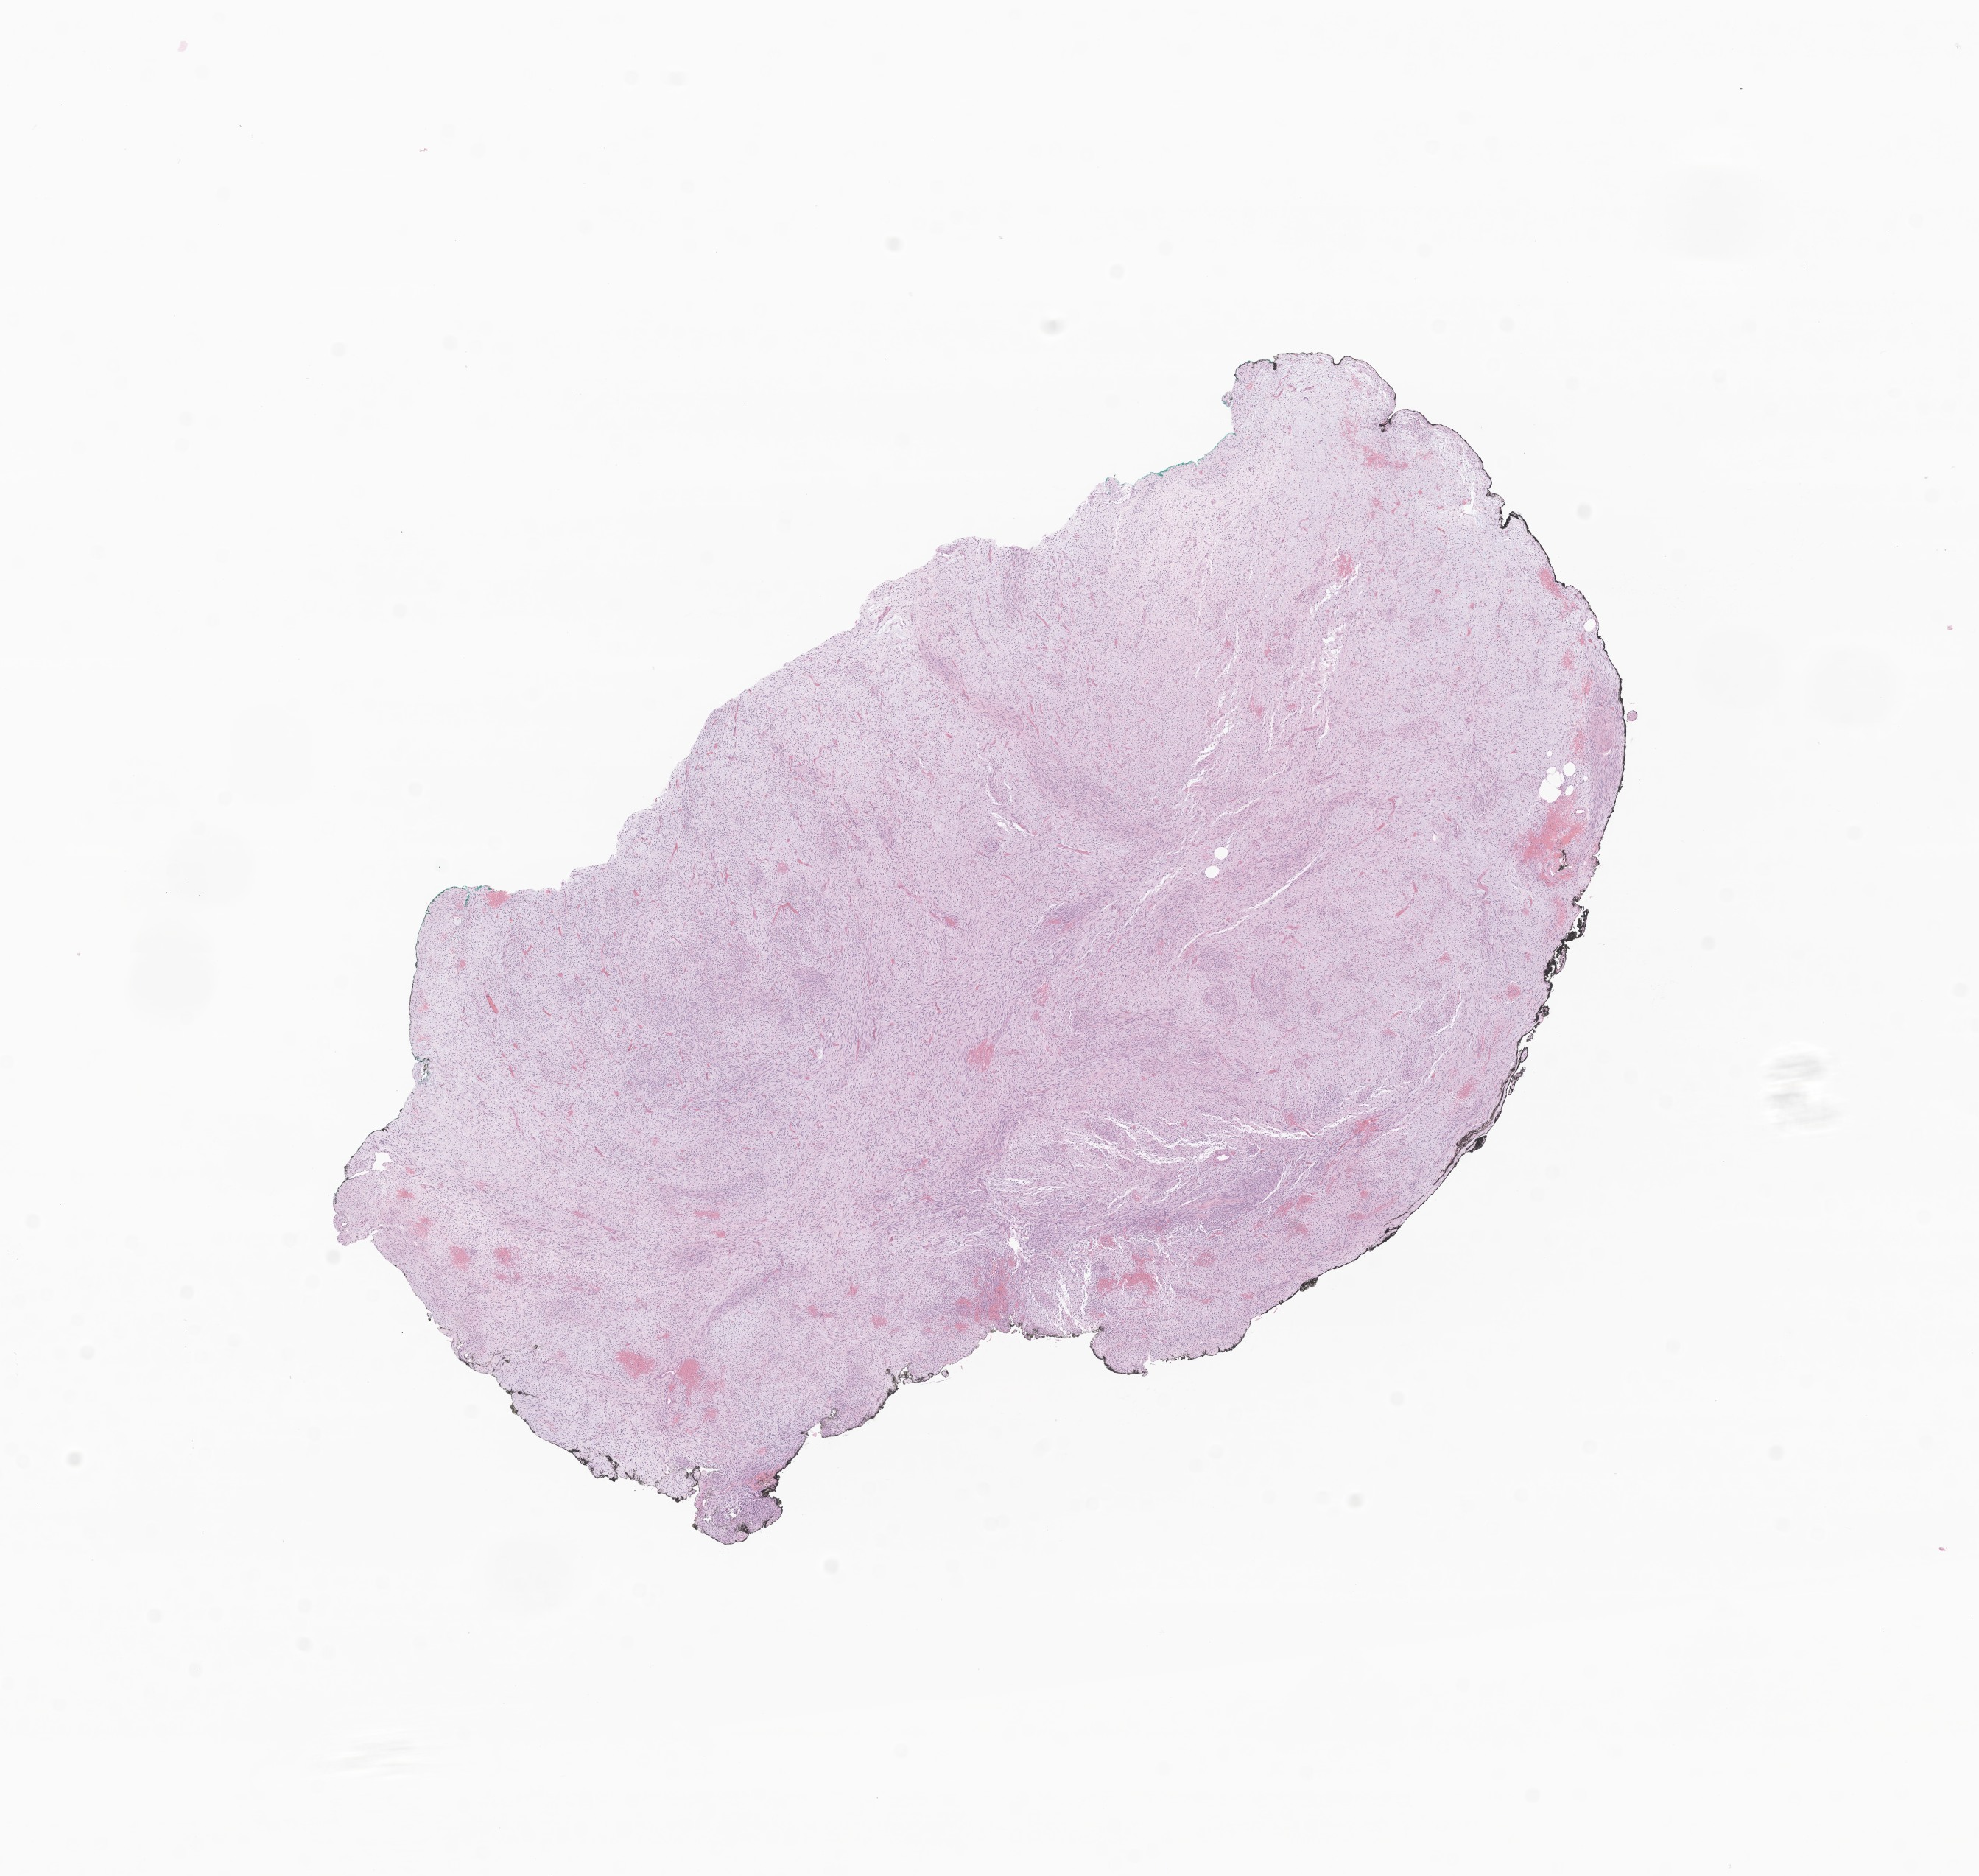
Digitized haematoxylin and eosin-stained section of tumor tissue from the soft tissue of upper extremity, whole scanned area (about 11.3 x 10.7 mm) shown as a low-resolution overview, formalin-fixed, paraffin-embedded (FFPE) tissue. Patient female; age 182 months (15 years 2 months).
• diagnosis: Synovial sarcoma, spindle cell